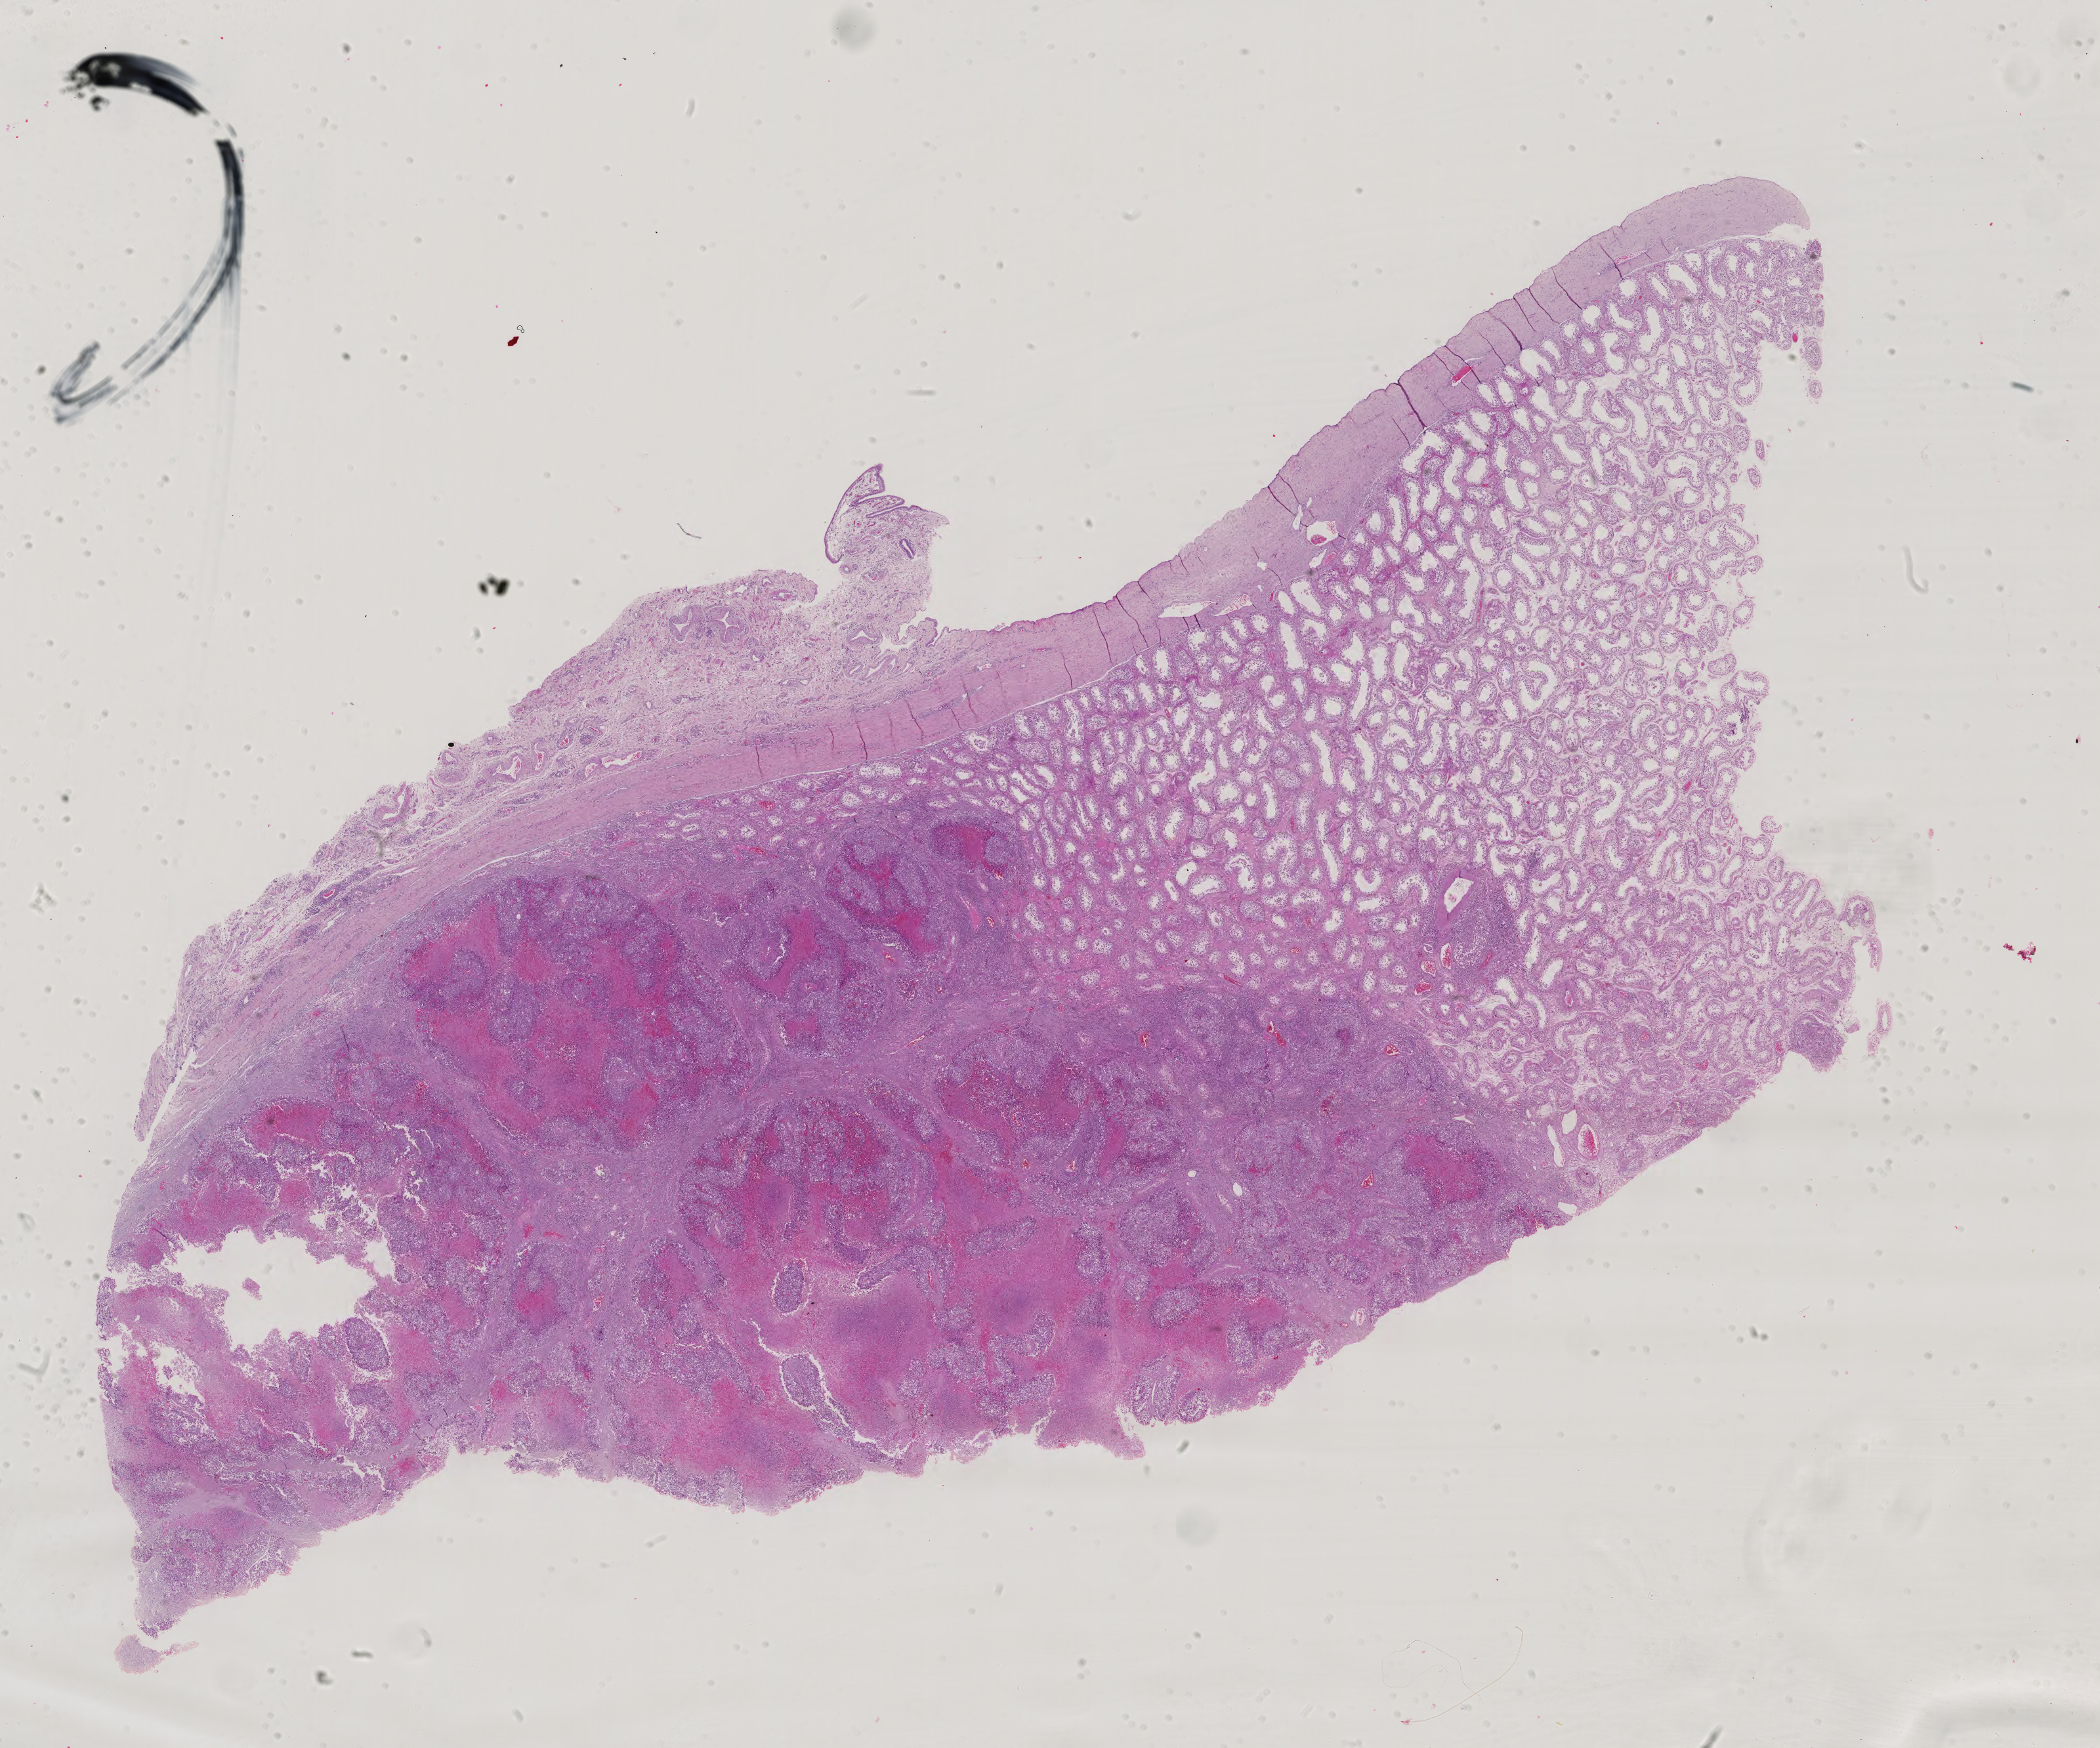
Digitized Hematoxylin and eosin (H&E) stained tissue section (whole slide), whole scanned area (about 23.3 x 19.4 mm) shown as a low-resolution overview. FFPE section. Testis, primary tumour sample. Male, age 32 years at initial diagnosis.
Histologic diagnosis: Embryonal carcinoma, NOS.